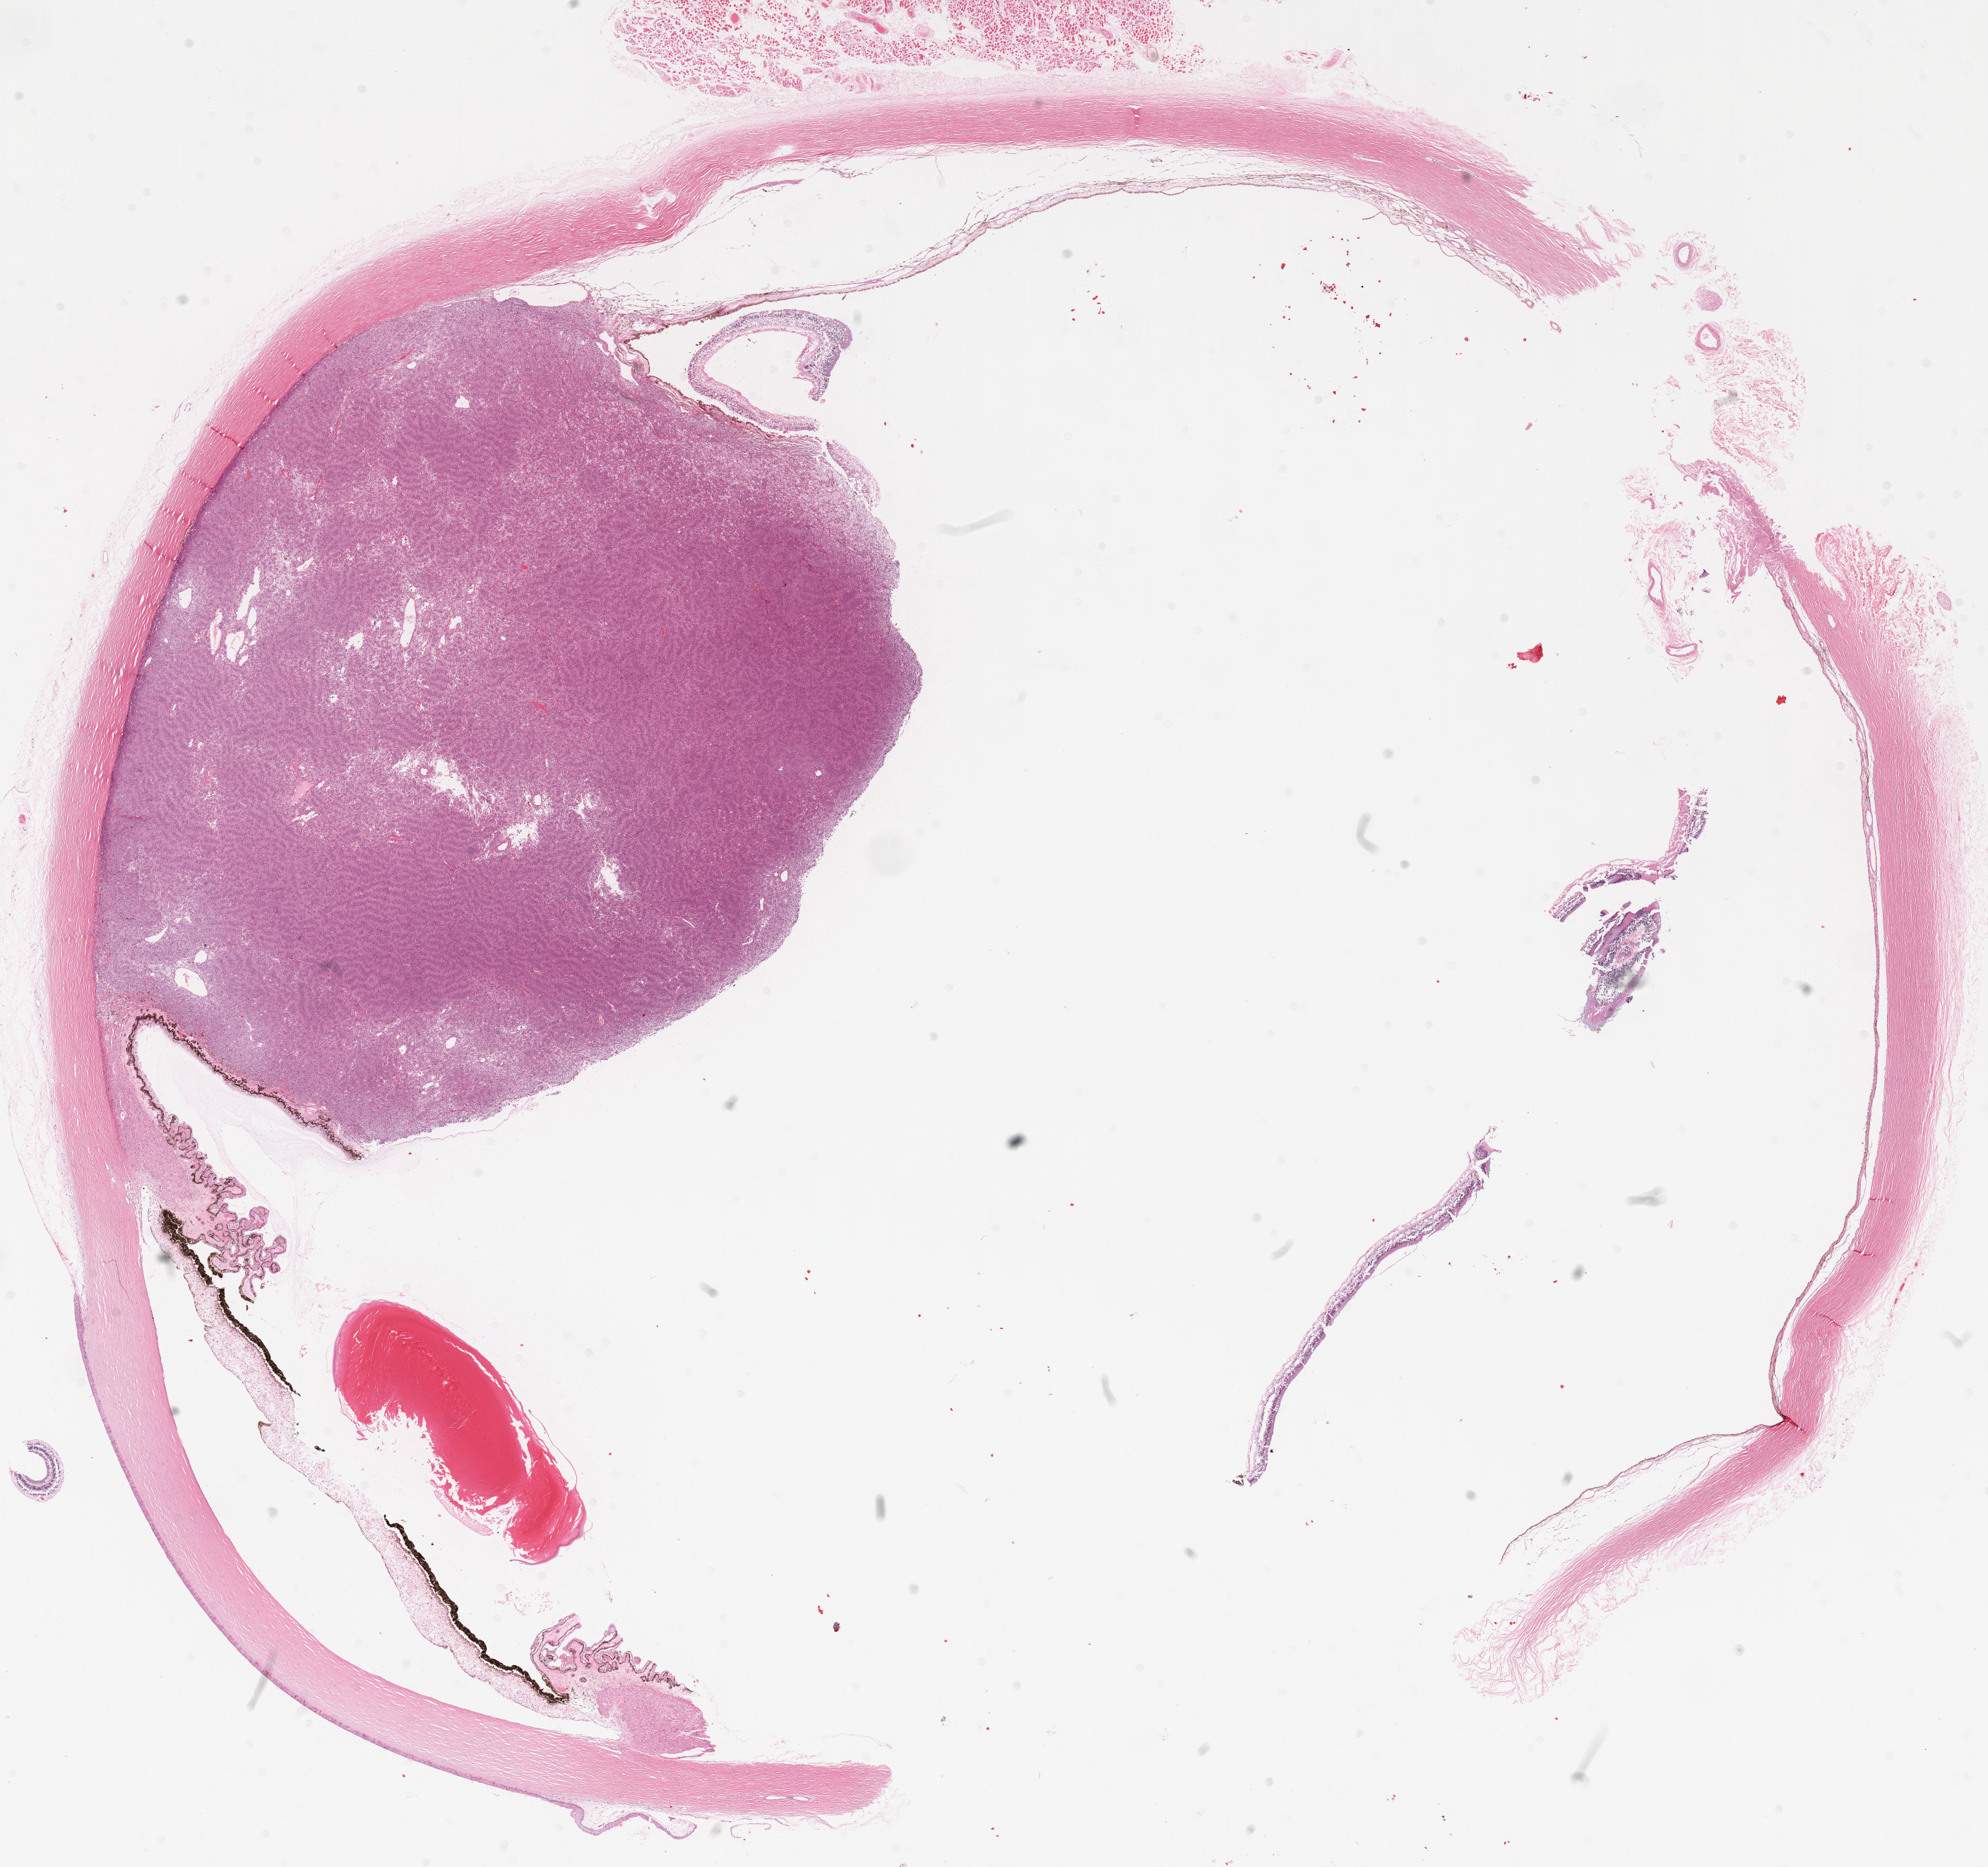
Whole-slide histology image, H&E-stained, a low-resolution overview of the entire scanned area, about 22.7 x 21.3 mm; formalin-fixed paraffin-embedded (FFPE) diagnostic section; sample: primary tumour, uvea. Female, age 78 years at initial diagnosis. Pathologist review of this section (percent, as recorded): tumour cells 75%, tumour nuclei 75%, normal cells 5%, stromal cells 20%, necrosis 0%. Inflammatory infiltration, as recorded: lymphocyte infiltration 4%, monocyte infiltration 1%, neutrophil infiltration 3%.
AJCC pathologic stage: IIB. Histologic diagnosis: Mixed epithelioid and spindle cell melanoma (choroid).